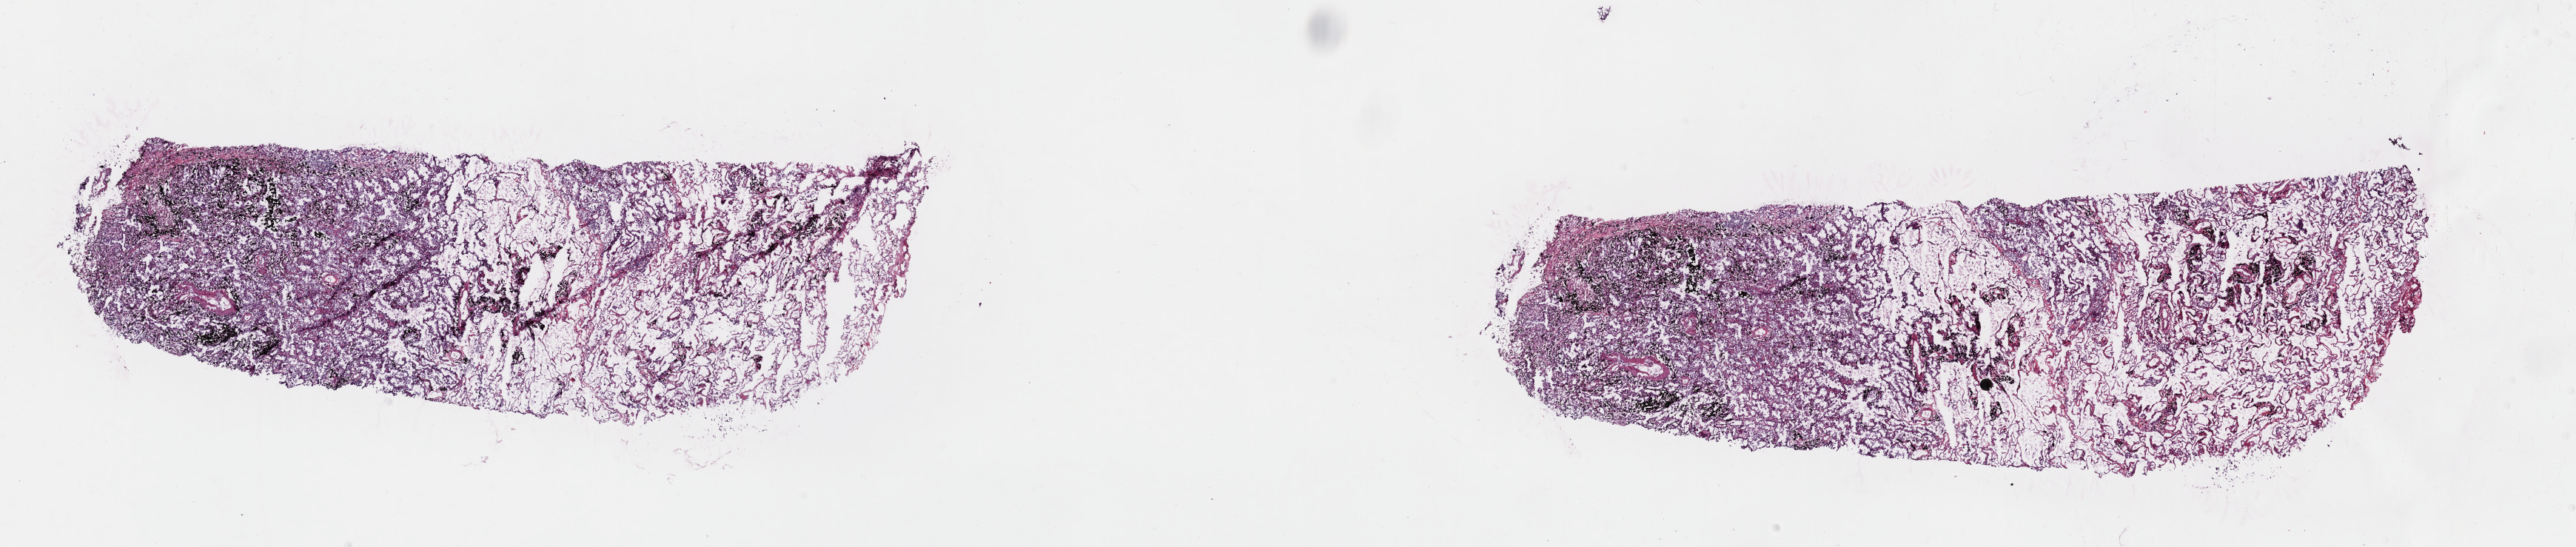
H&E whole-slide image, a low-resolution overview of the entire scanned area, about 27.5 x 5.8 mm (slide scanned at 40x); frozen section from the top of the tissue portion; sample: primary tumour, lung. Female patient; age at initial diagnosis 78 years. Pathologist review of this section (percent, as recorded): tumour cells 80%, tumour nuclei 100%, normal cells 0%, stromal cells 20%, necrosis 0%. Infiltration values recorded for this section: lymphocyte infiltration 2%, monocyte infiltration 3%, neutrophil infiltration 0%.
- AJCC pathologic stage: IA (7th edition)
- diagnosis: Papillary adenocarcinoma, NOS (upper lobe, lung)